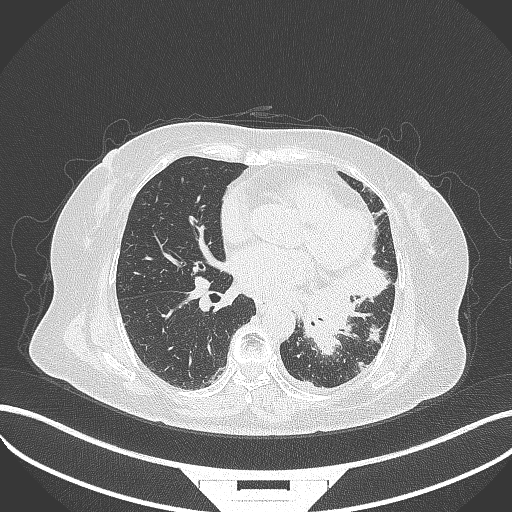
Chest CT, one axial slice. Position 160 of 322 along the scan axis. Reconstruction kernel B70f. 120 kVp. Lung window (W 1500 / L -600 HU). 1 mm slice thickness. 512 × 512 image matrix, field of view 400 × 400 mm. Patient: female, 69 years. Case-level facts recorded for this patient, not image findings: clinical TNM (as recorded): T2b N3 M1.
Structures marked on this image (bounding box drawn by a radiologist):
- lung tumour (recorded histology: adenocarcinoma): bounding box [x1, y1, x2, y2] px = [299, 282, 356, 359]